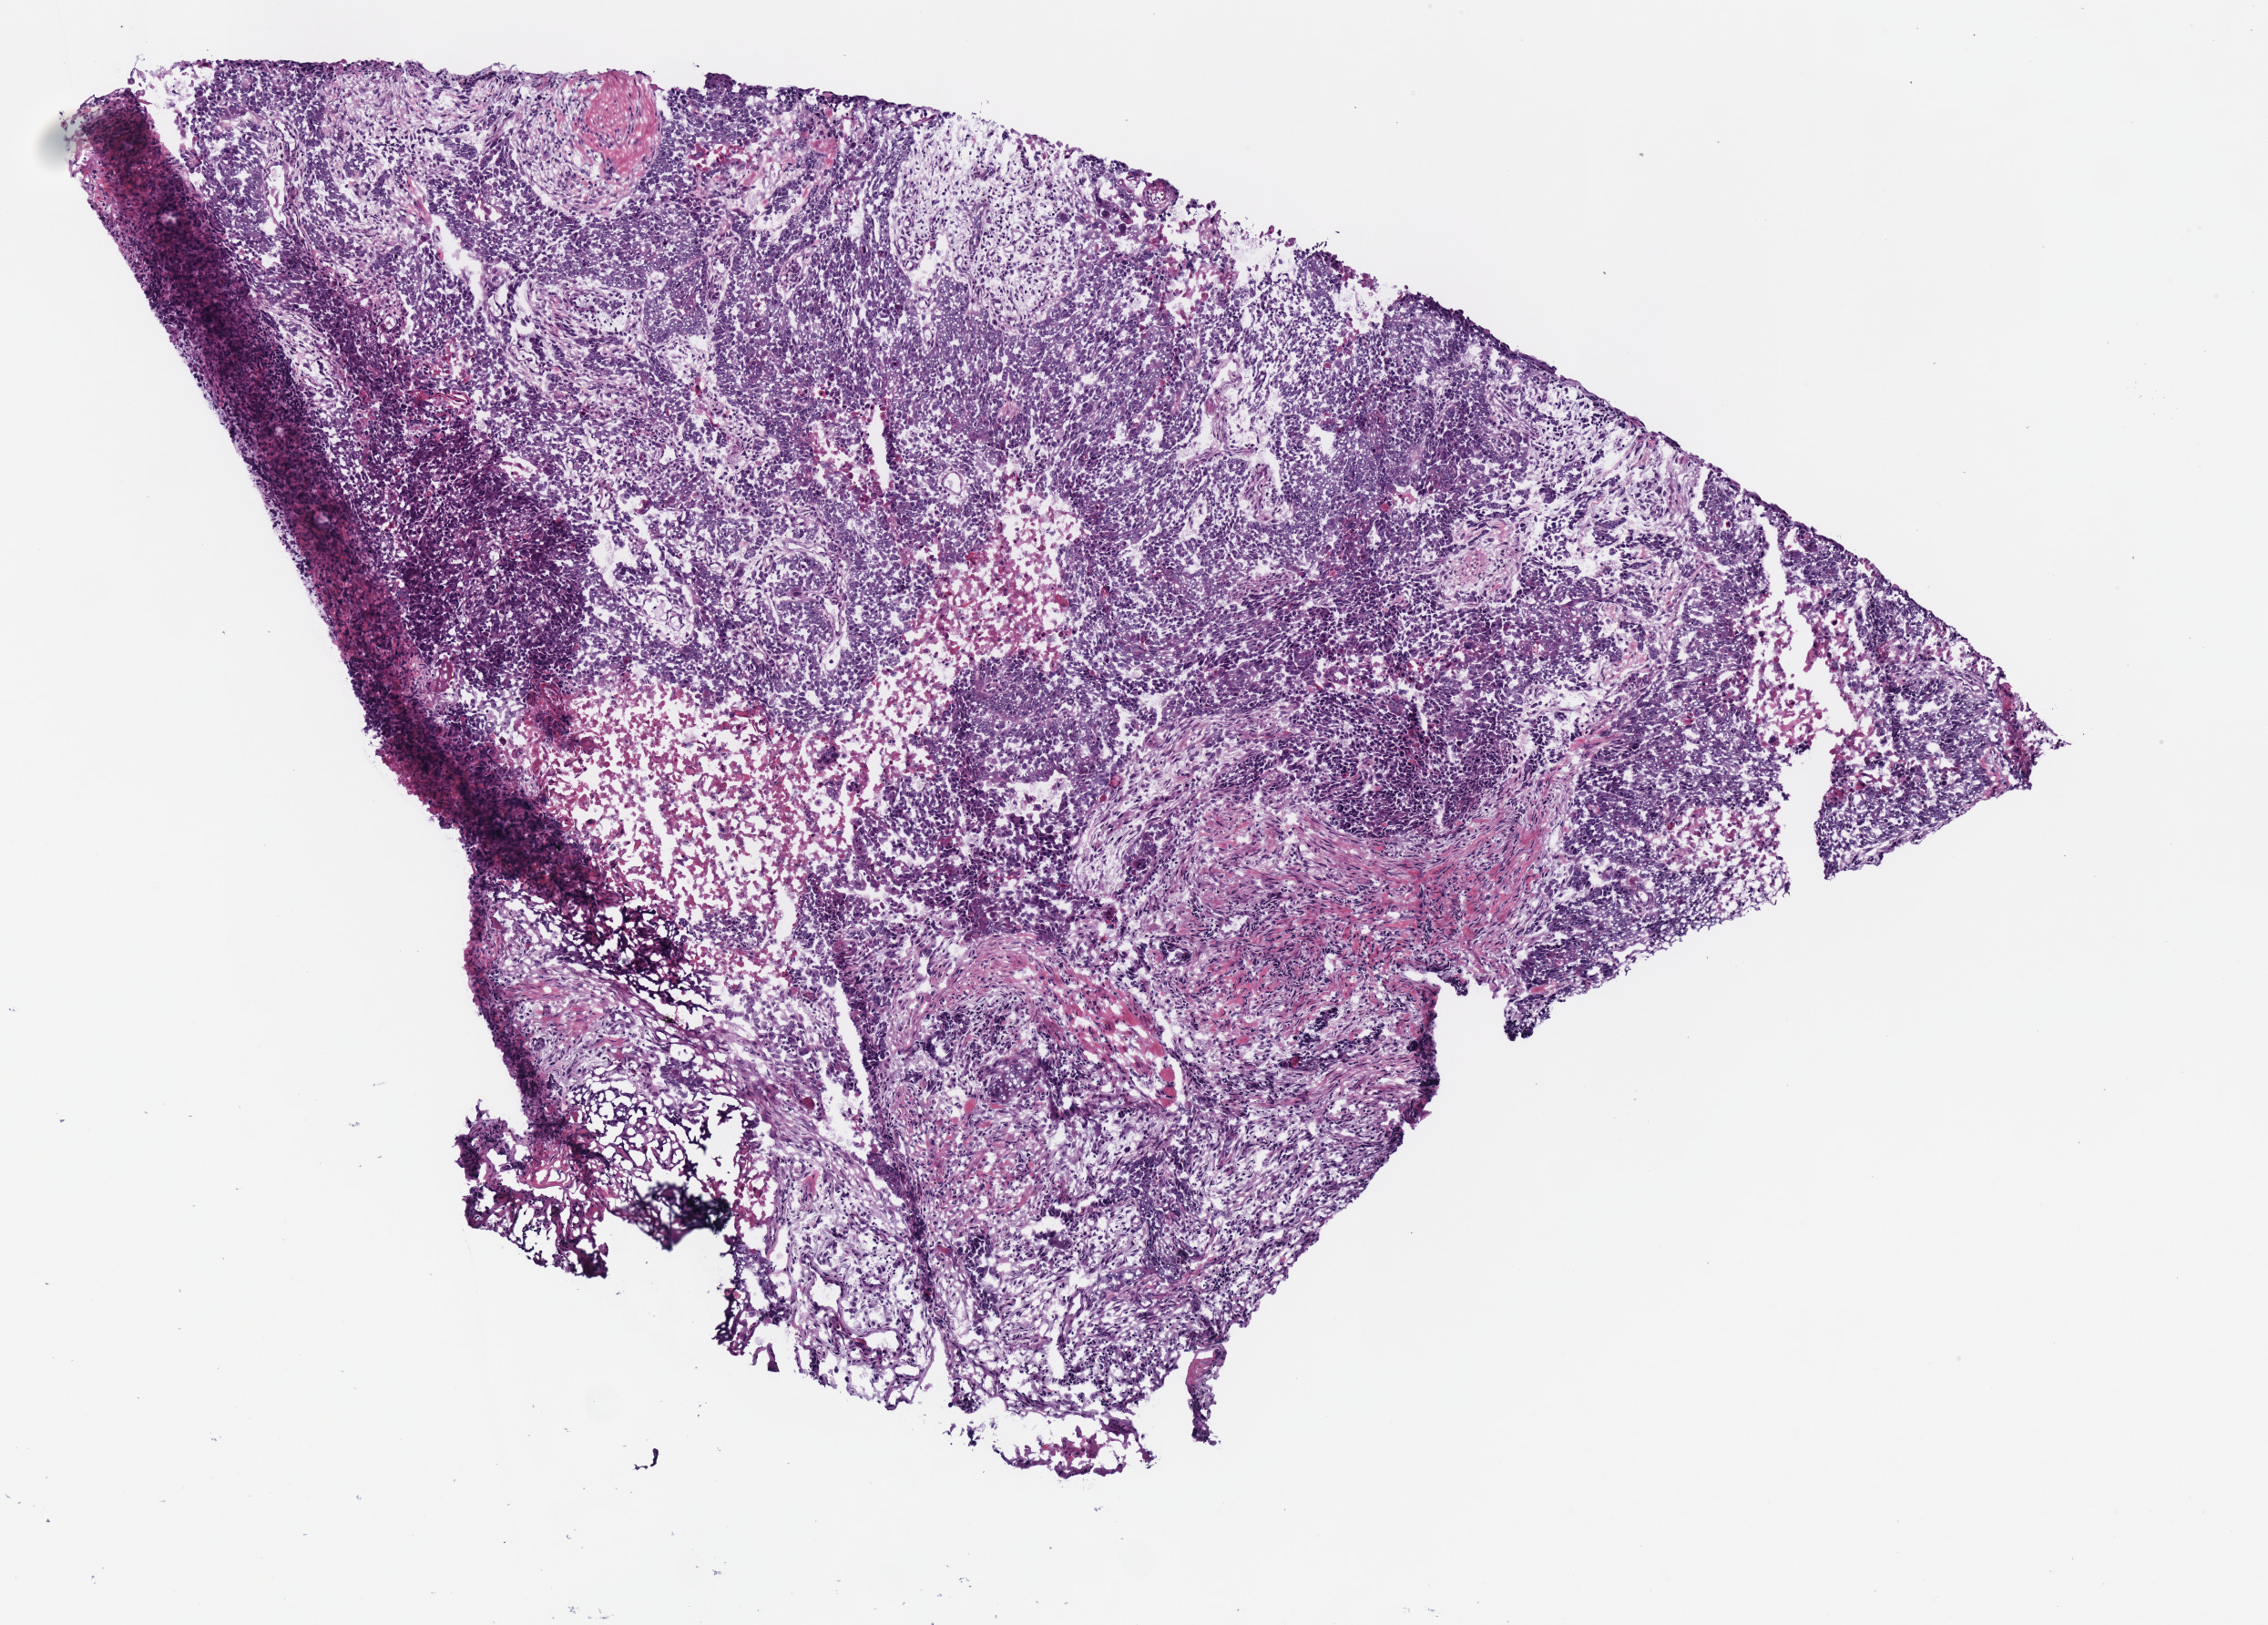
H&E-stained whole-slide image, shown as a low-resolution overview of the whole scanned area (about 4.9 x 3.5 mm, acquisition: 40x scan), frozen section, sample: primary tumour, head and neck. Male, age 67 years at initial diagnosis. Histologic grade: G3 (poorly differentiated). Composition of this section per pathologist review: tumour cells 75%, tumour nuclei 75%, normal cells 0%, stromal cells 10%, necrosis 15%.
AJCC pathologic stage: IVA (7th edition). TNM: T3 N2c. Histologic diagnosis: Squamous cell carcinoma, NOS (larynx, NOS).